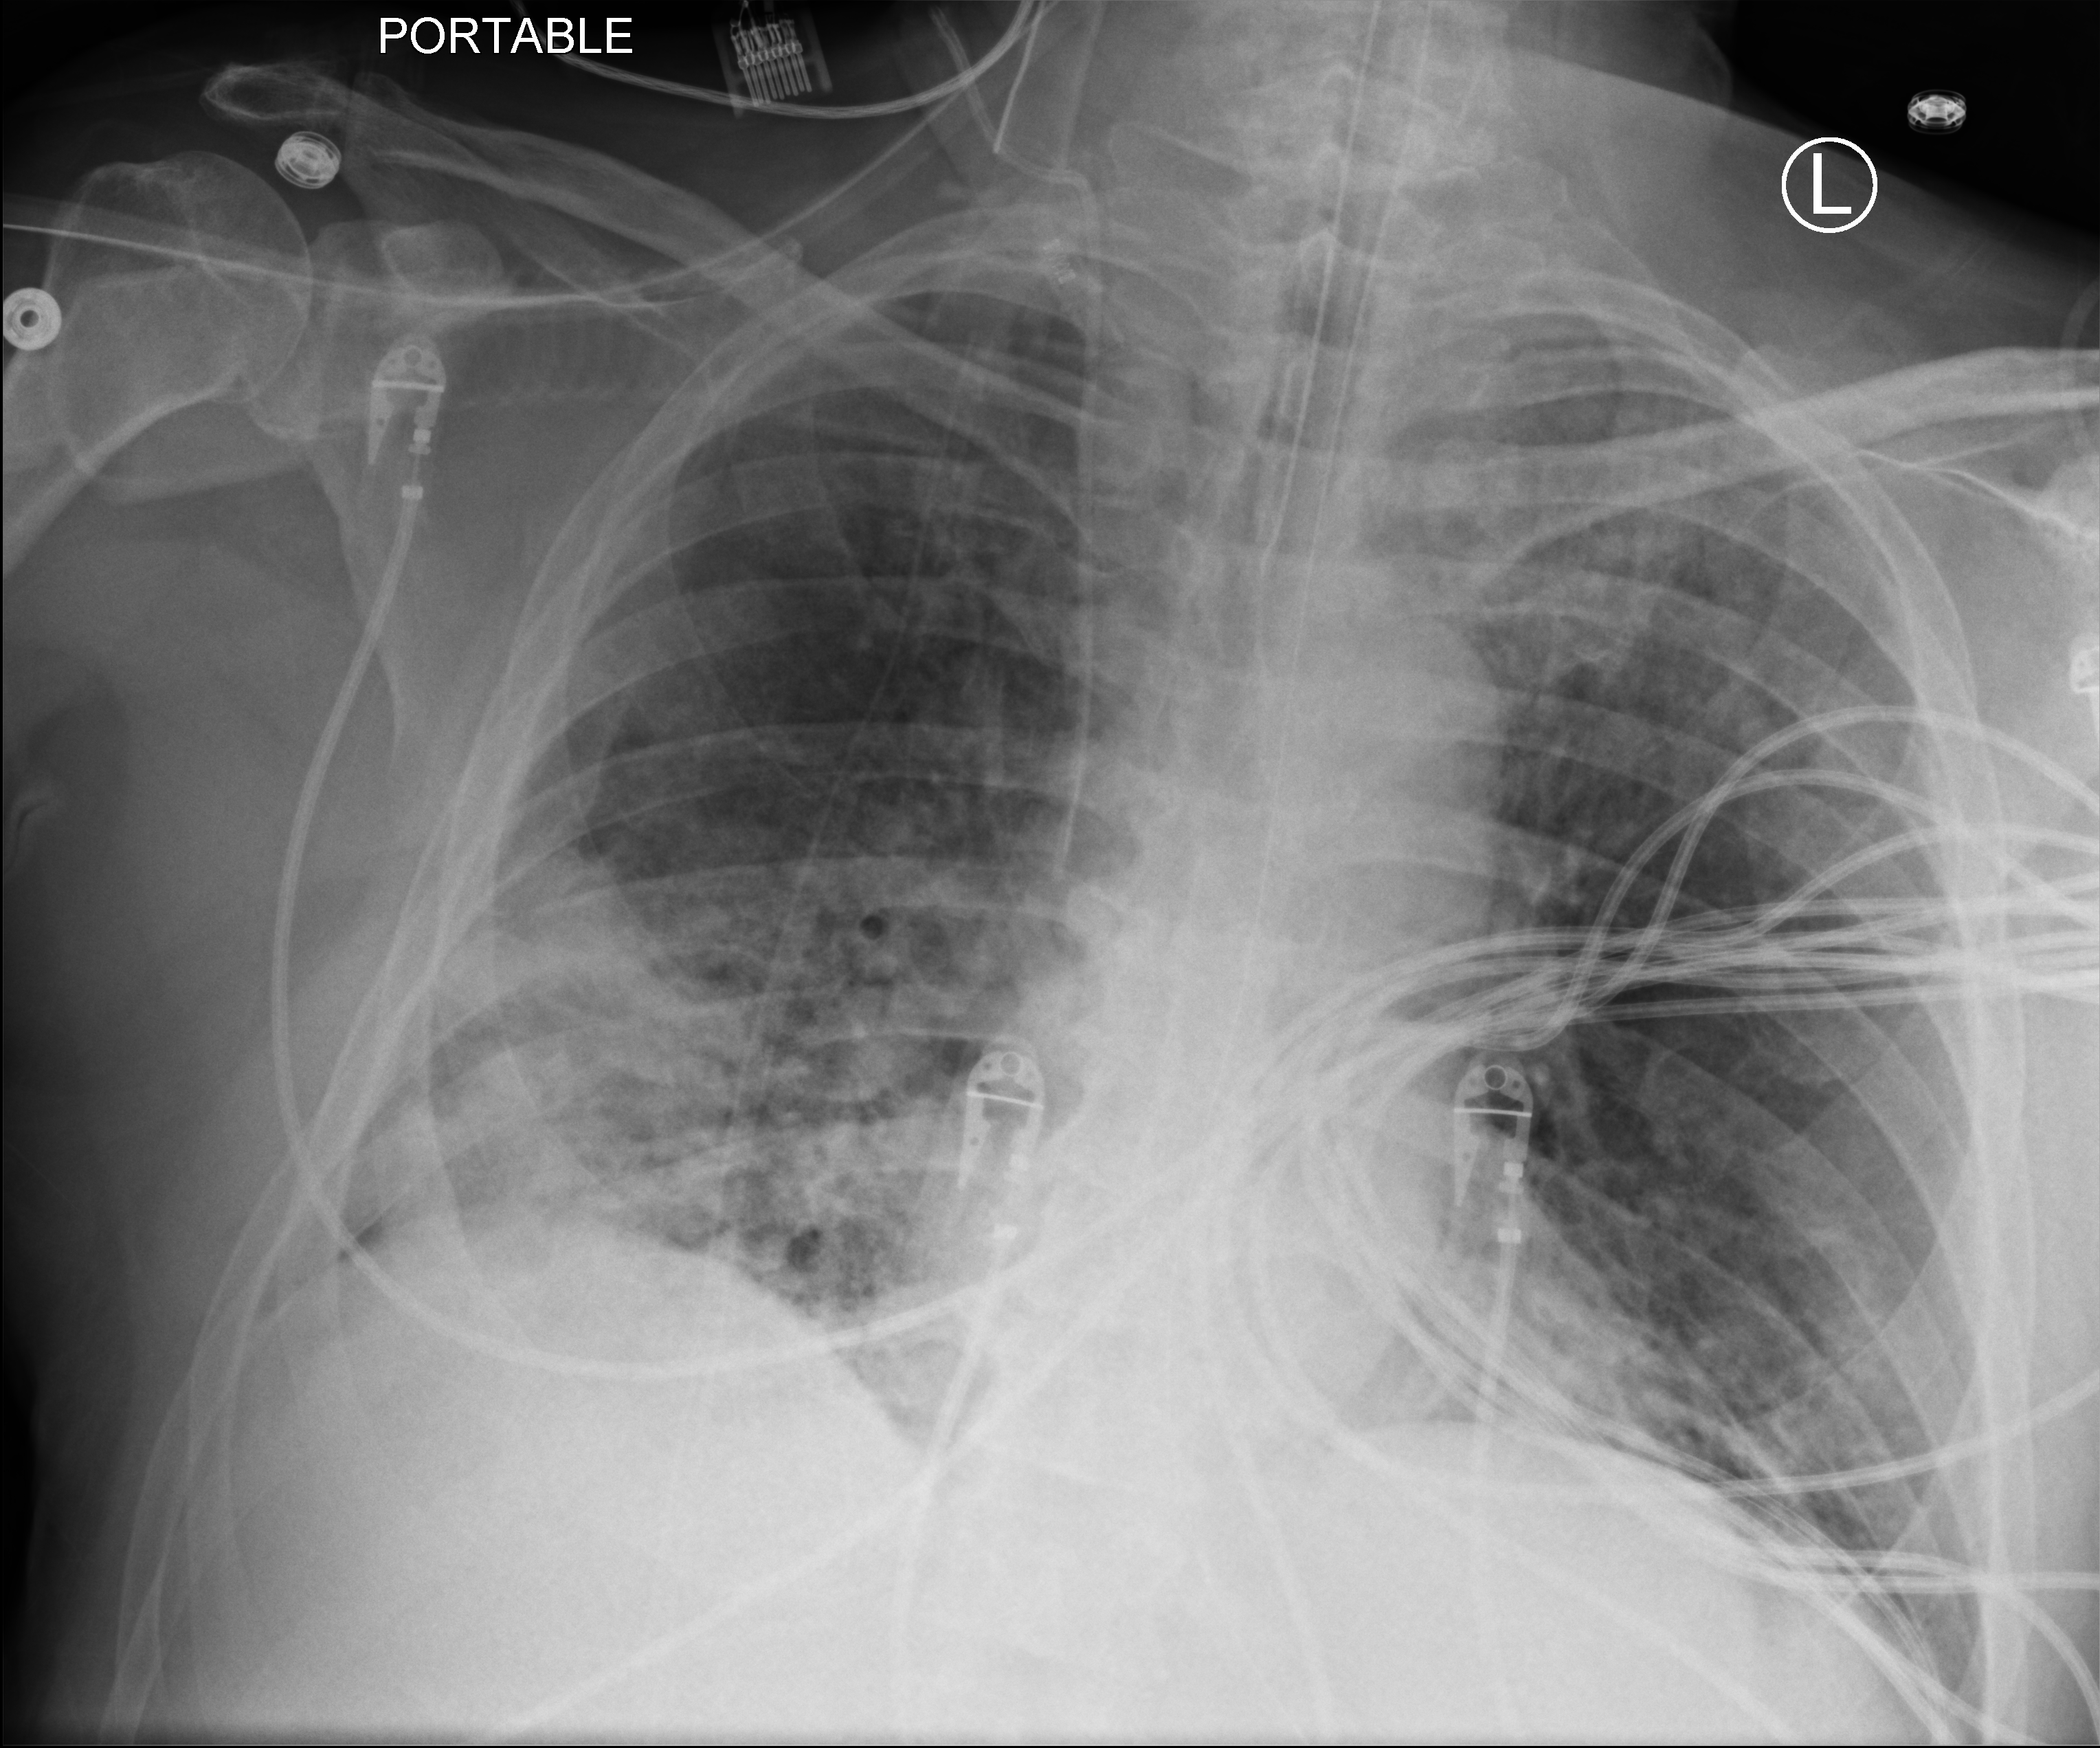
Chest X-ray (portable); anteroposterior (AP) projection. Male patient hospitalised with COVID-19, age 60–74 years.
Admission-level facts for this patient (not findings on this image; timing relative to this image not recorded):
- length of hospital stay: 33 days